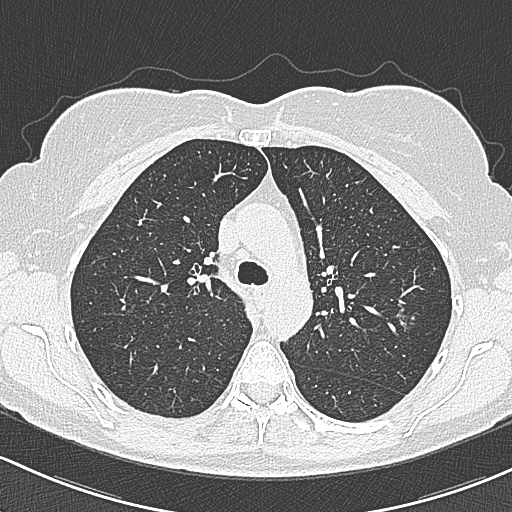
Low-dose screening chest CT, axial slice; baseline annual screen; lung window (W 1500 / L -600 HU); 1 mm slice thickness; lung (sharp) reconstruction kernel (B80f); slice 93 of 312 in the series; 512 × 512 image matrix. Female participant, aged 65 years at enrolment. Current smoker at enrolment.
Expert reader's lesion annotation, bounding box (x1, y1, x2, y2) in pixels: (388, 301, 426, 337). The screening reader recorded 3 non-calcified nodules or masses ≥4 mm on this exam (left upper lobe, left upper lobe, right upper lobe); which of them this box marks is not recorded. Official screen result: positive, change unspecified: nodule(s) >= 4 mm or enlarging nodule(s), mass(es), or other non-specific abnormalities suspicious for lung cancer. Participant outcome: lung cancer diagnosed 390 days after this screen (after the second annual screen) — bronchiolo-alveolar carcinoma, non-mucinous, left upper lobe, stage IA (AJCC 6th edition), 10 mm at pathology.